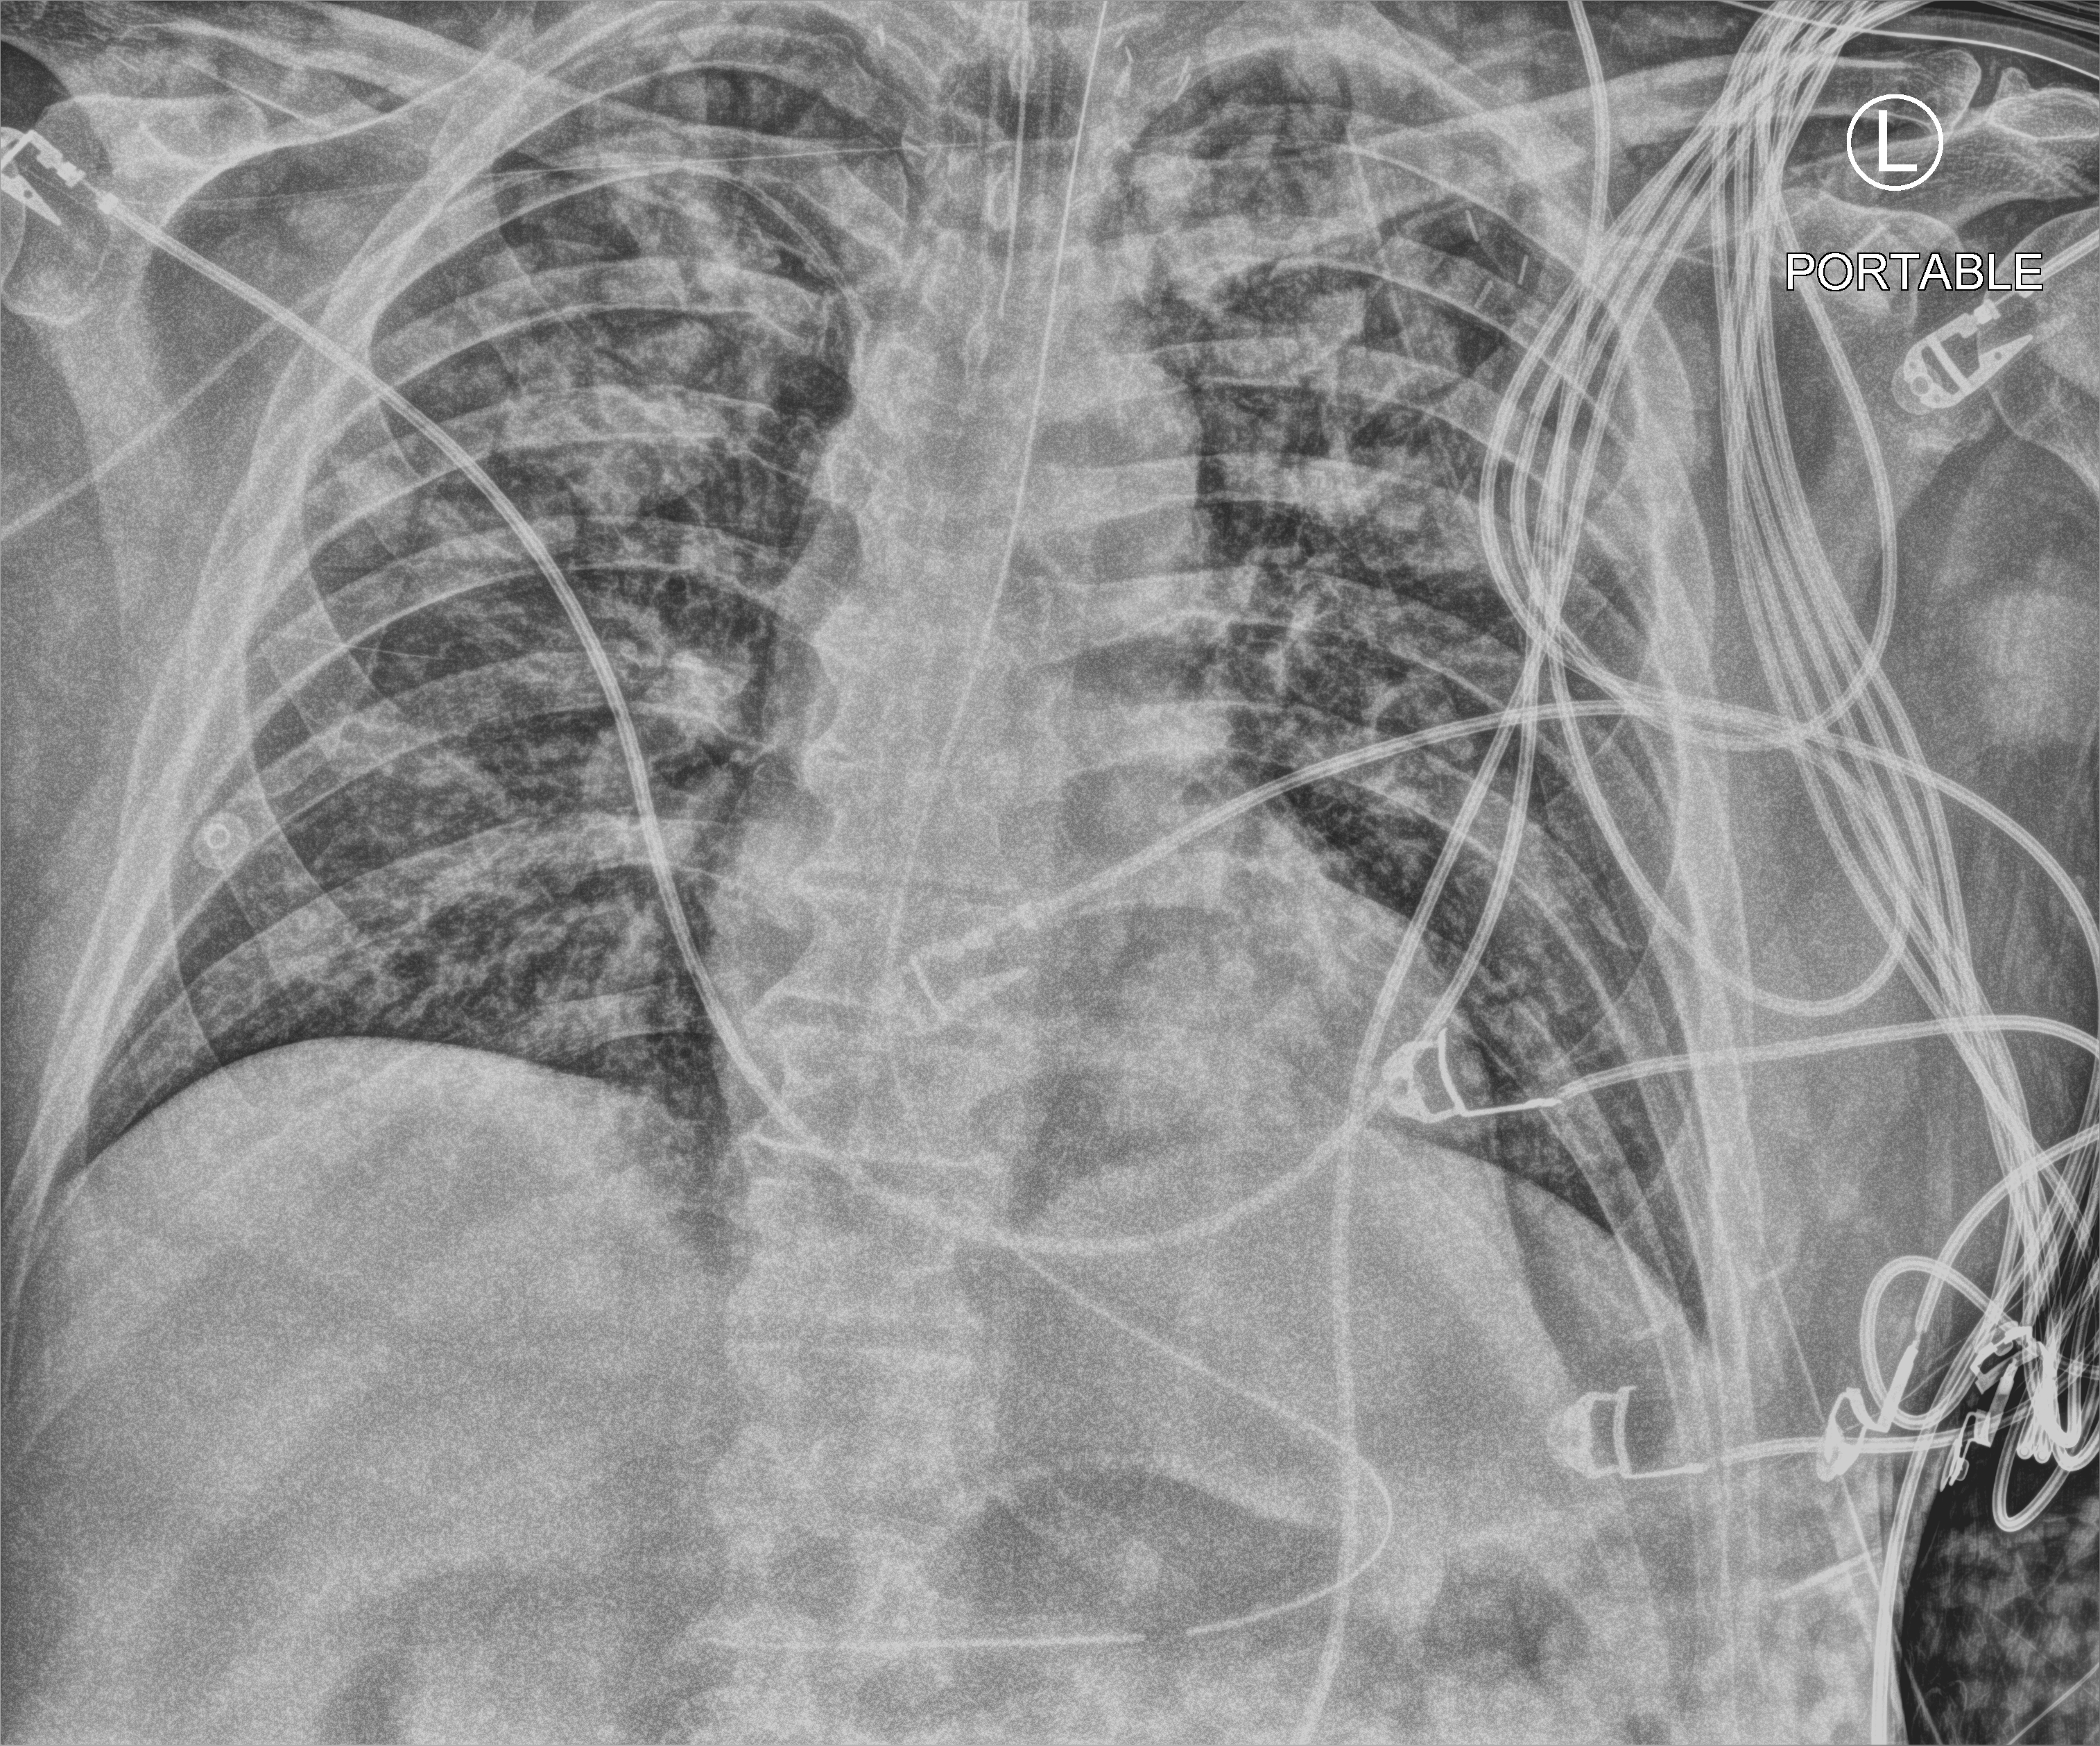
Chest X-ray (portable), anteroposterior (AP) projection. Adult patient hospitalised with COVID-19, age 18–59 years.
From the hospital-stay record, not from the radiograph (when in the stay this image was taken is not recorded):
- length of hospital stay: 19 days
- COPD (admission record): no
- mechanically ventilated during this hospital stay: yes